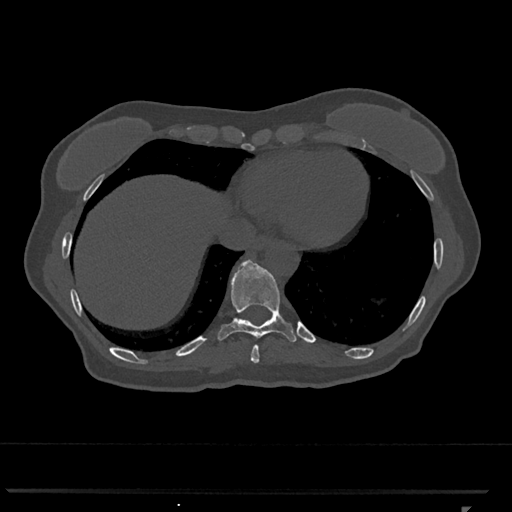
CT including the spine, one axial slice. Slice 573 of 793 in the series (ordered by position). Reconstruction kernel Br40s/3. 120 kVp. Bone window (W 1800 / L 400 HU). 512 × 512 image matrix. Patient: female, 62 years. From the clinical record (not read from this slice): primary cancer: renal.
Outlined on this slice (semi-automatic segmentation, software-assisted and operator-edited):
- T10 vertebra: bounding box <217,260,297,342> (left, top, right, bottom; pixels)
- T9 vertebra: <251,345,259,363>